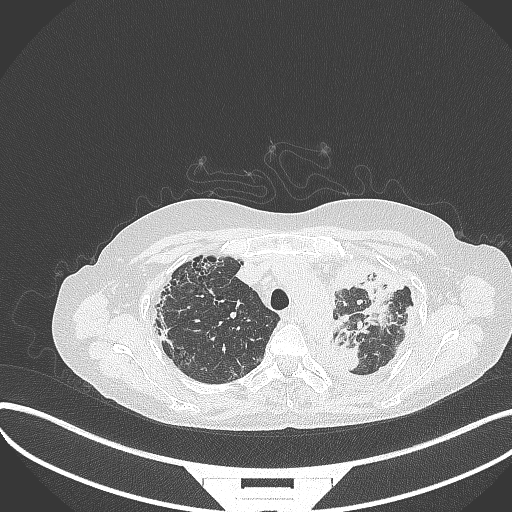
Chest CT, one axial slice; lung window (W 1500 / L -600 HU); 512 × 512 image matrix. Female patient, age 56 years. From the clinical record (not read from this slice): clinical TNM (as recorded): T1 N0 M0.
Annotated regions visible in this slice (rectangle marked by the reading radiologist):
- lung tumour (recorded histology: adenocarcinoma): bounding box [x1, y1, x2, y2] px = [335, 338, 359, 374]
- lung tumour (recorded histology: adenocarcinoma): [356, 262, 399, 330]